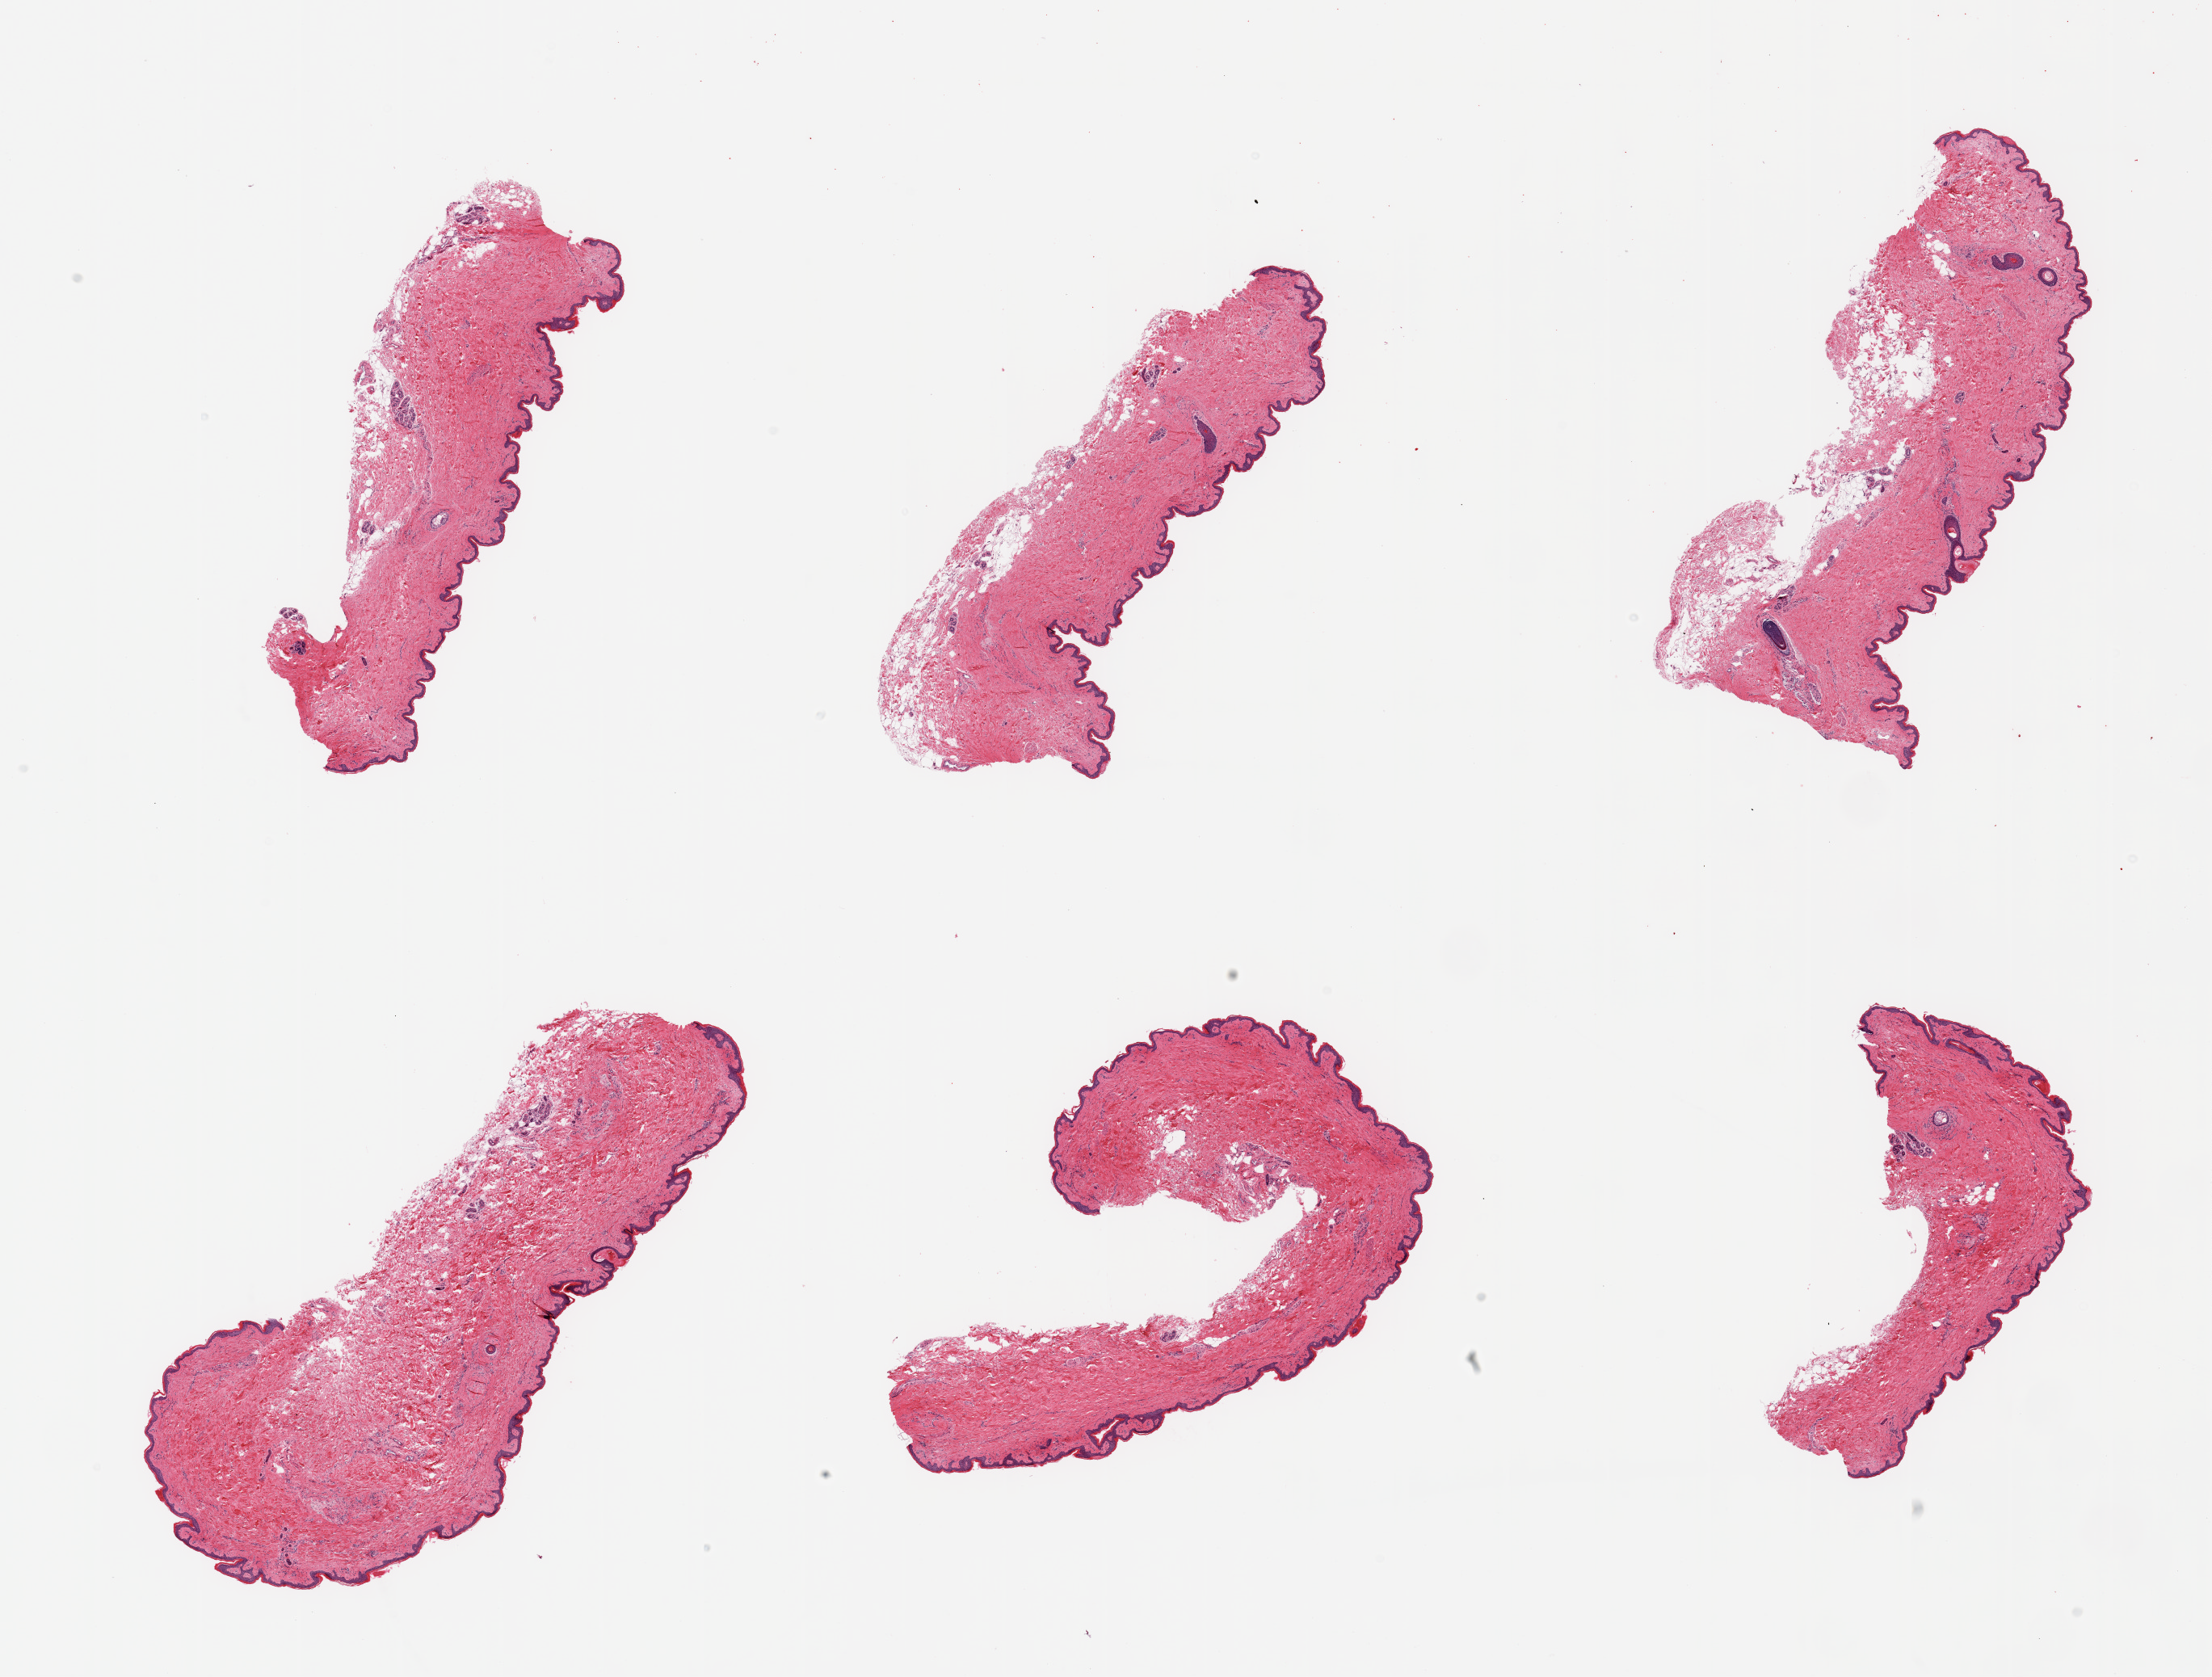
Whole-slide image, haematoxylin and eosin stain, brightfield — shown as a low-resolution overview of the whole scanned area (about 21.7 x 16.4 mm, slide scanned at 20x); PAXgene-fixed paraffin-embedded (PFPE) section; target tissue: skin of suprapubic region; tissue donor sample. Donor sex: female.
Reviewer comment on this tissue sample: 6 pieces; up to 20% dermal fat in 3 of 6 pieces.